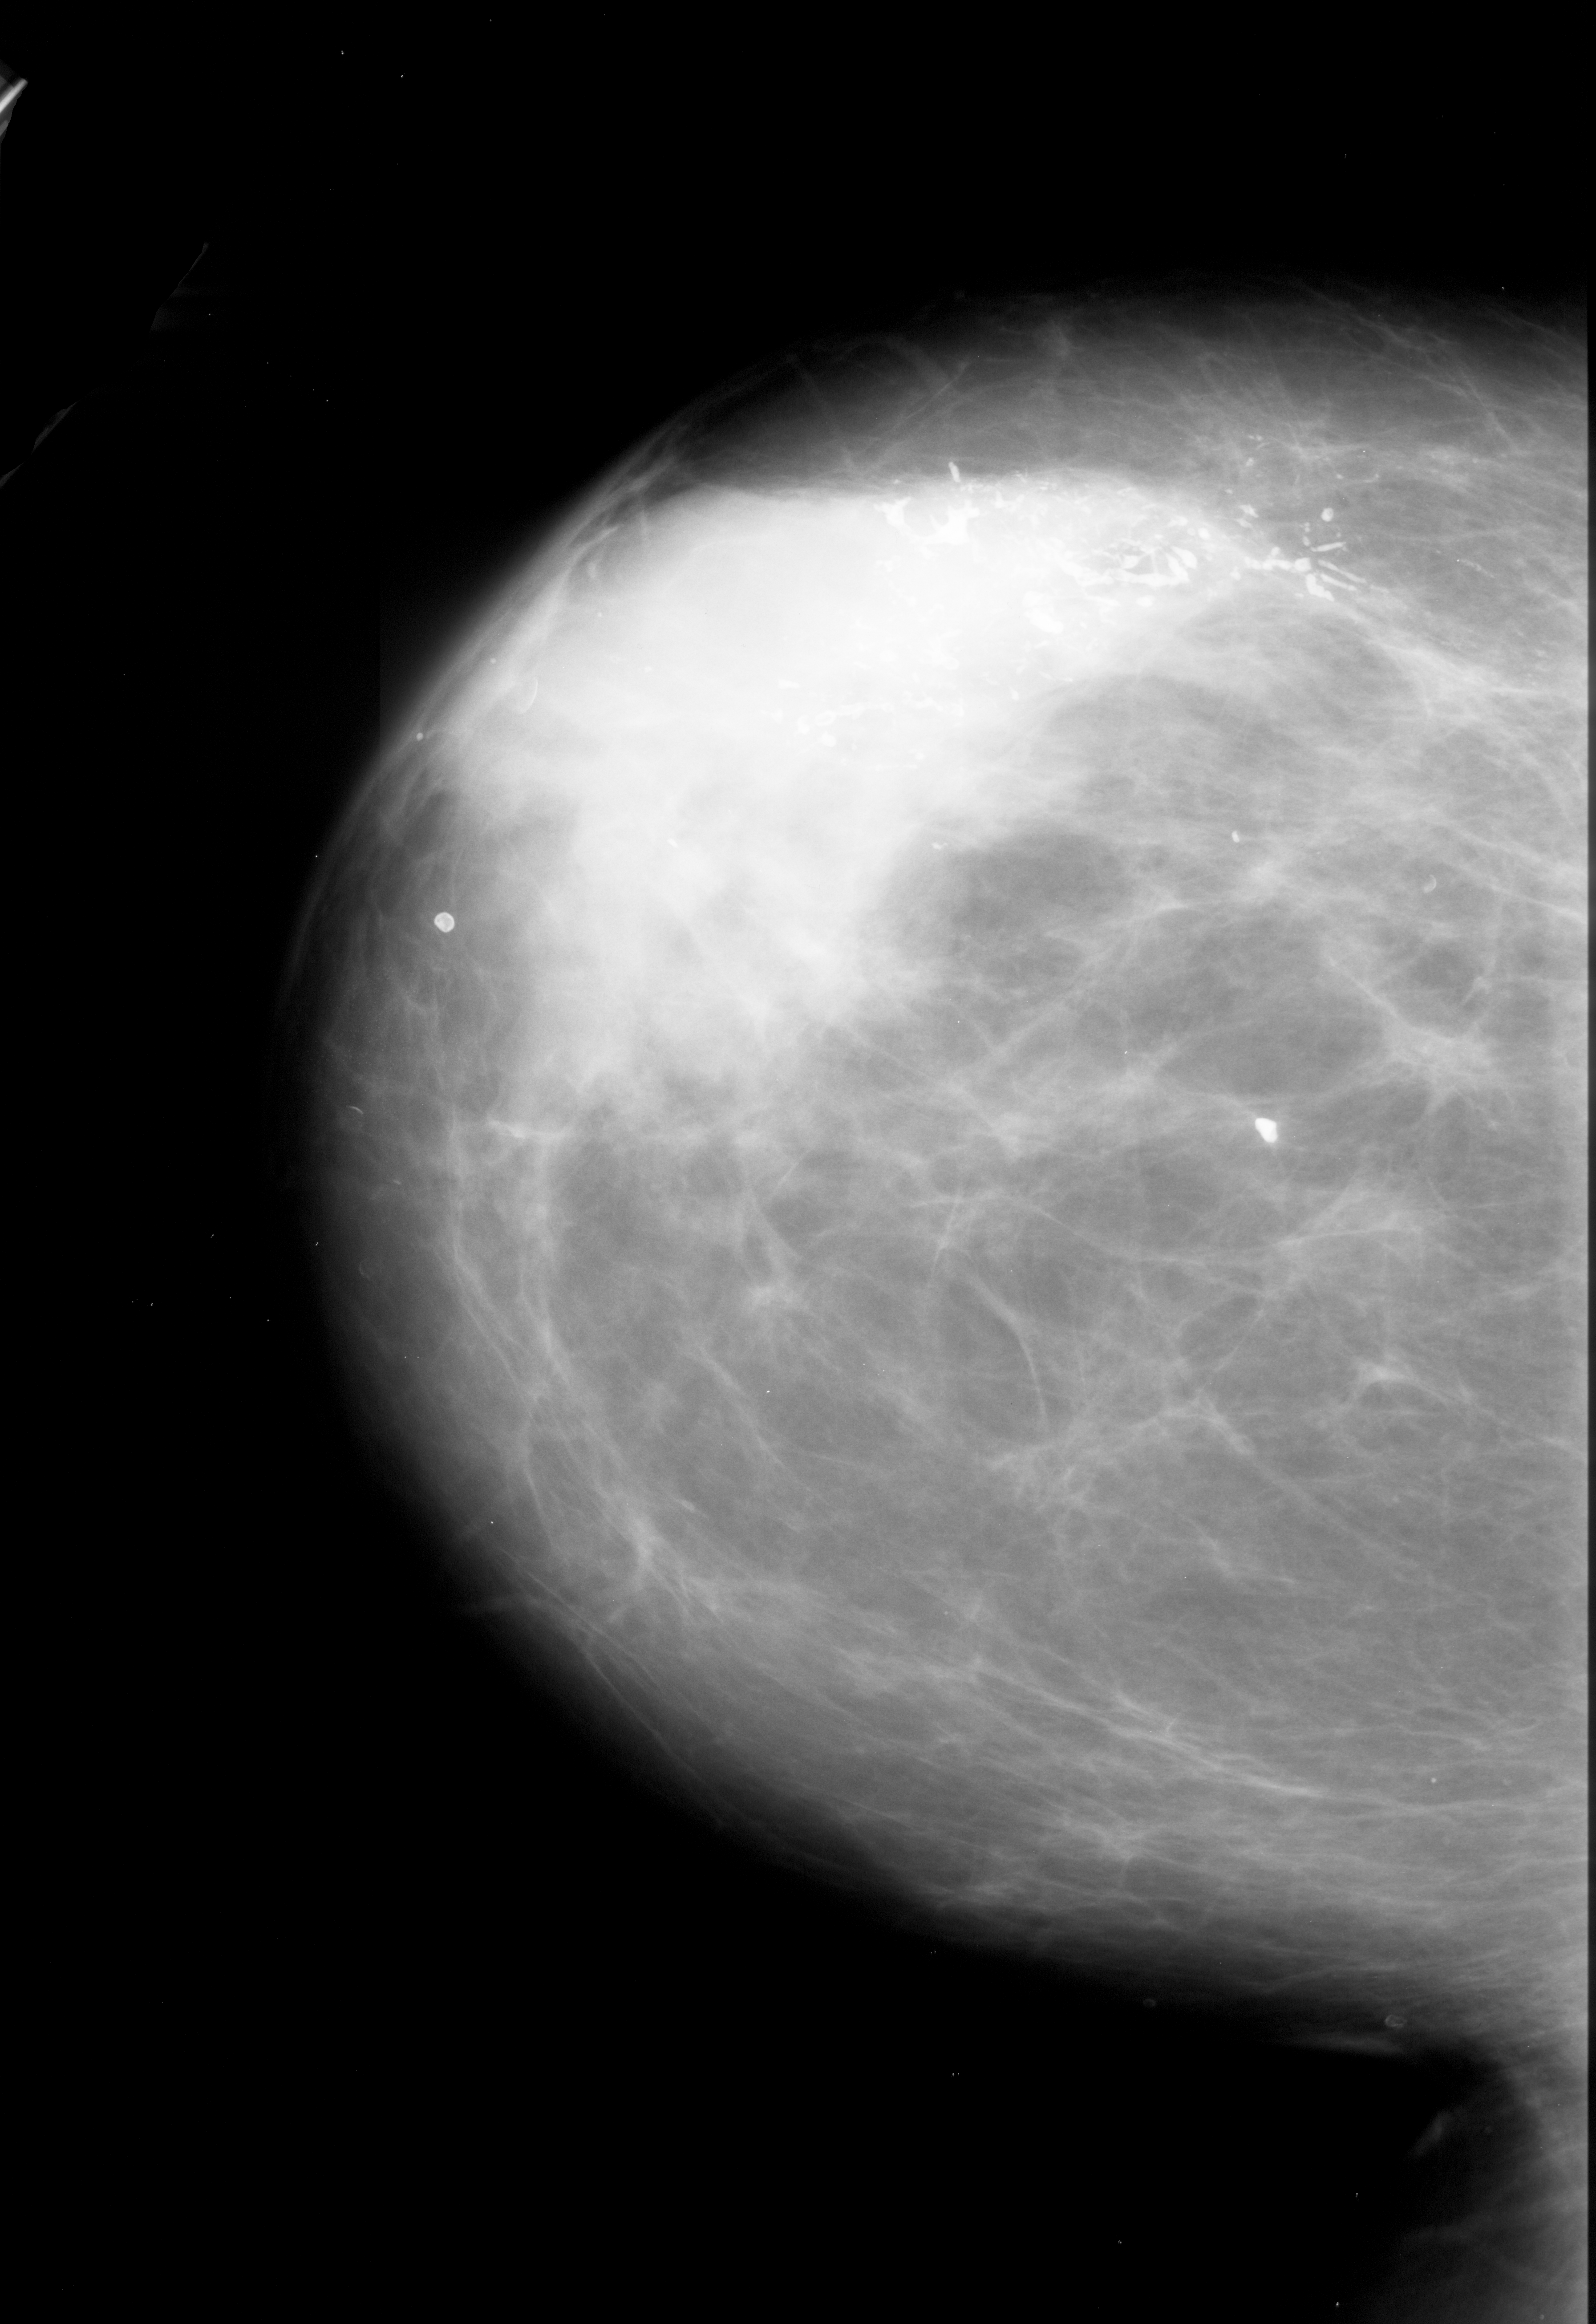
Mammogram (digitized film), left breast, craniocaudal (CC) view, BI-RADS breast density category 4 (scale 1–4).
Calcifications, morphology pleomorphic, distribution segmental; BI-RADS assessment category 5; pathology (as recorded): malignant.